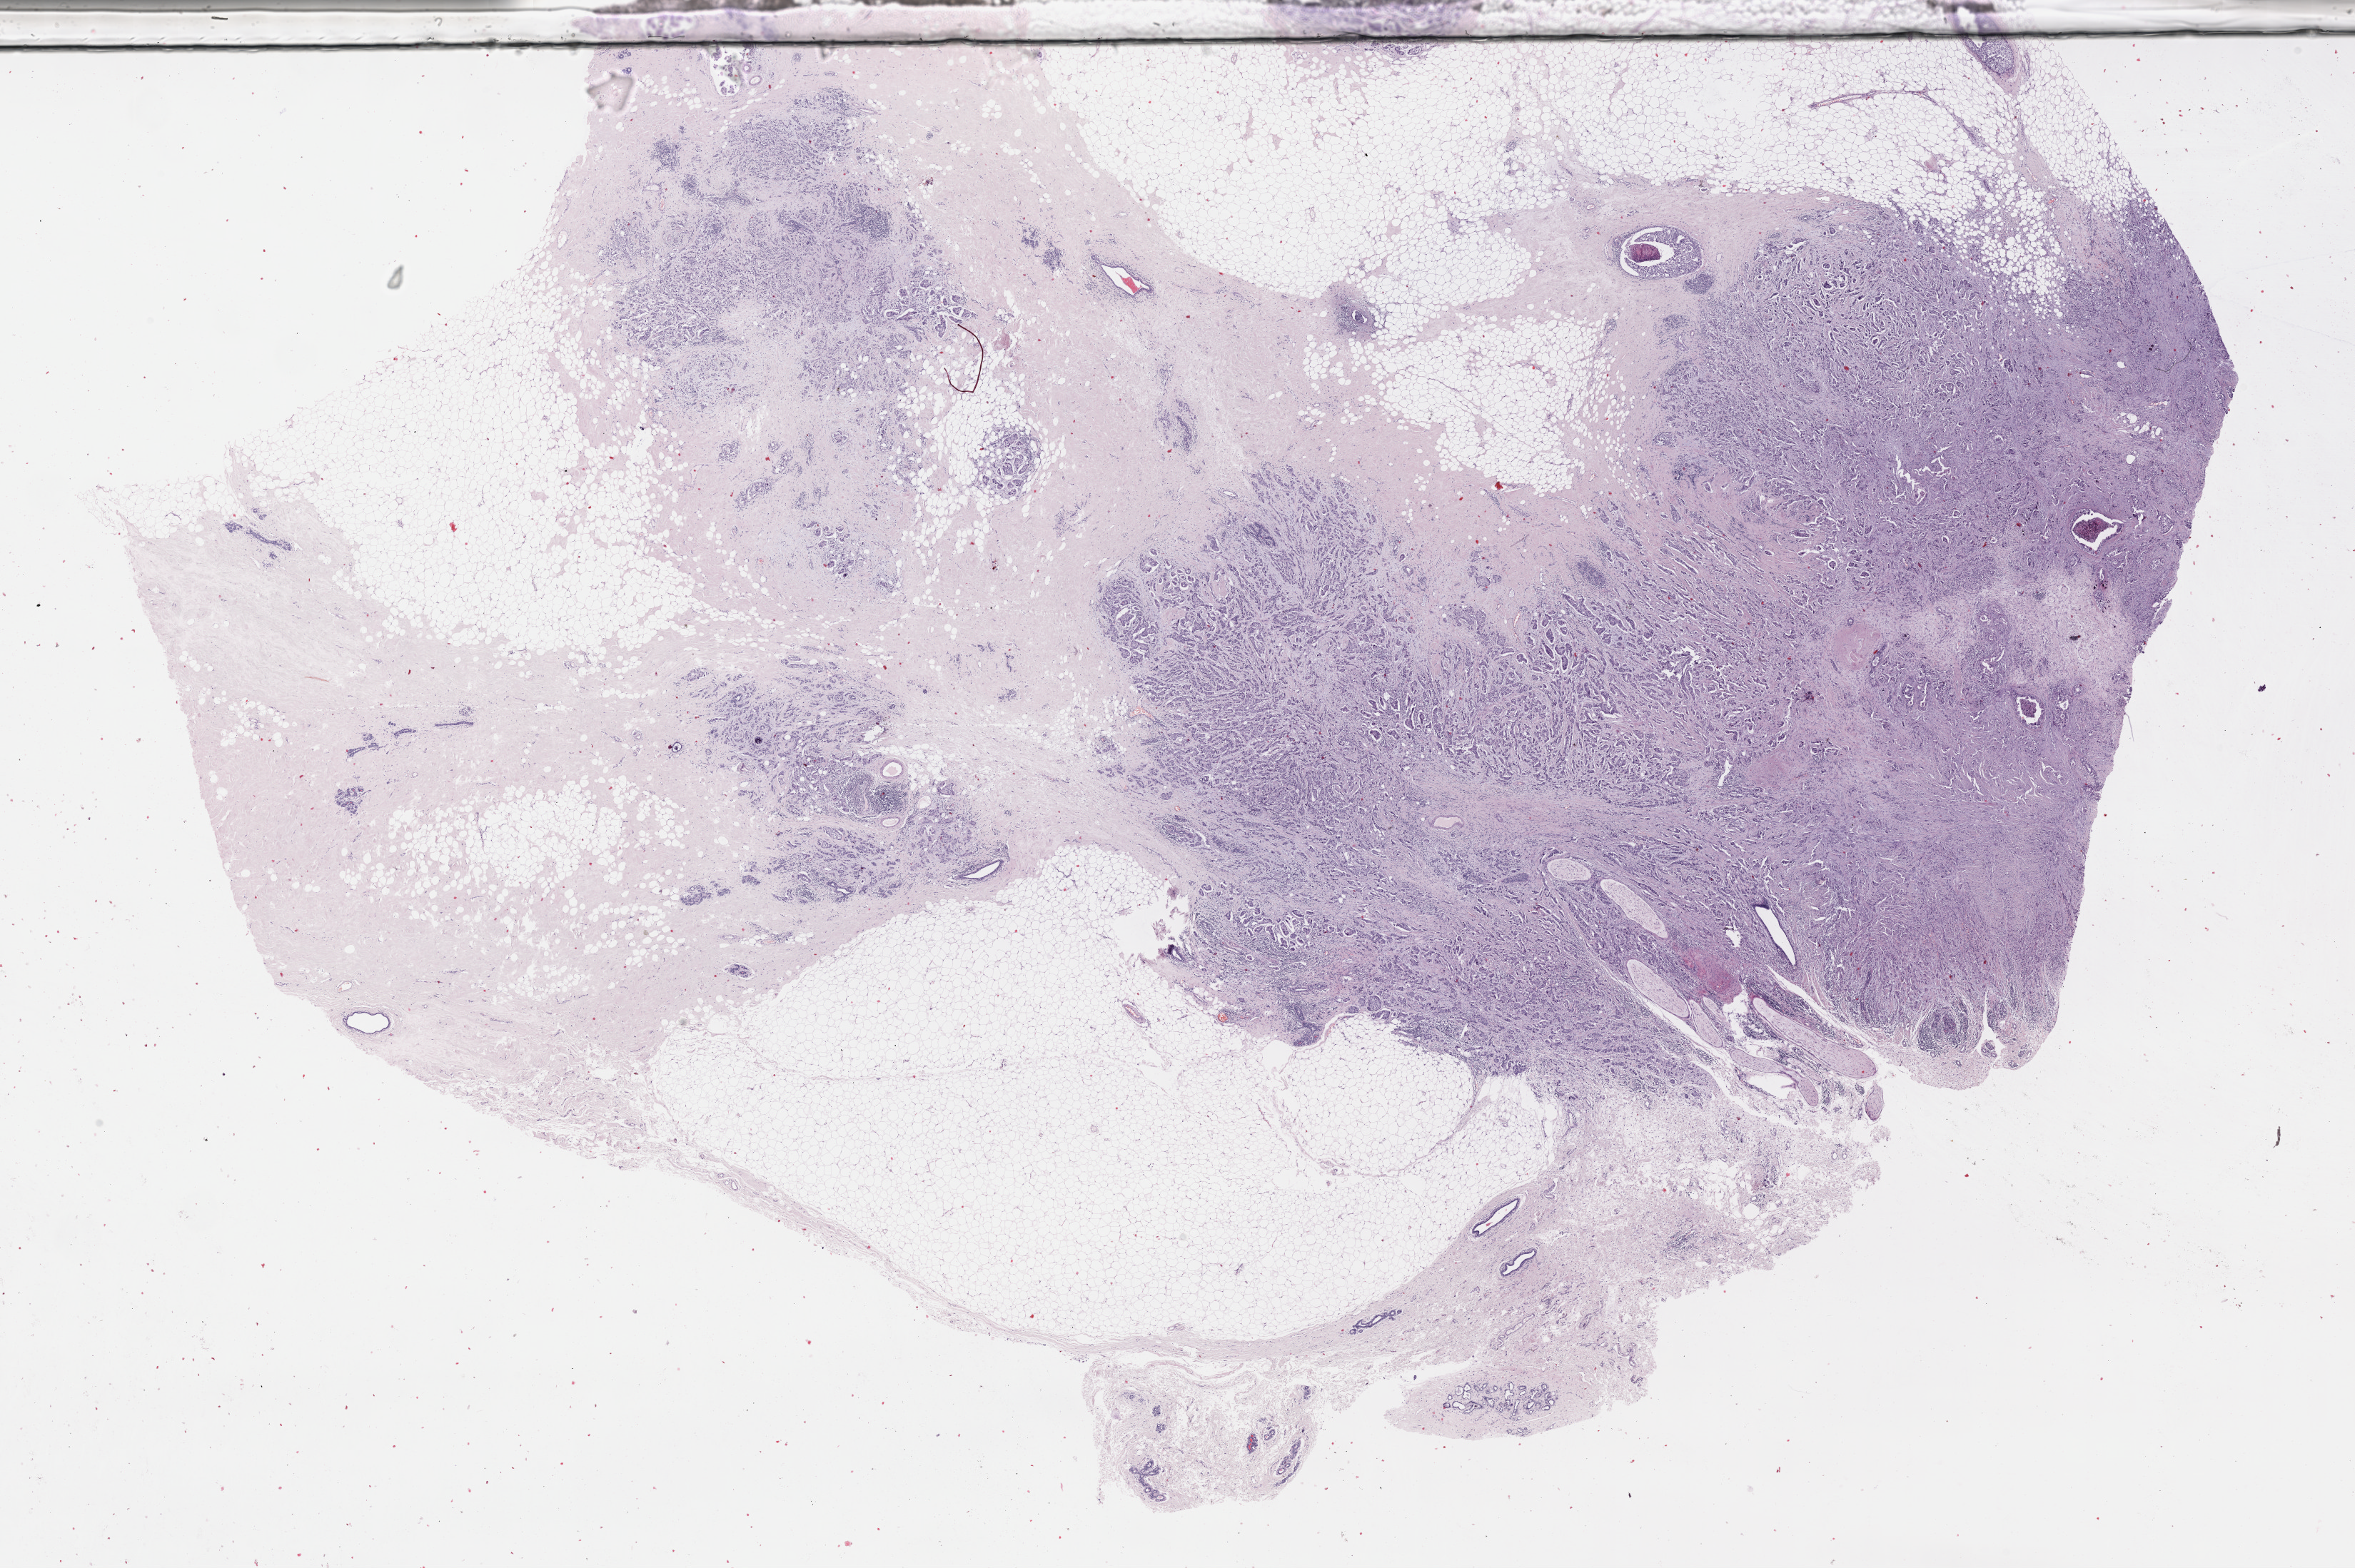
Whole-slide histology image, H&E-stained — a low-resolution overview of the entire scanned area, about 26.7 x 17.8 mm. Formalin-fixed paraffin-embedded (FFPE) diagnostic section. Primary tumour sample from the breast. Female, age 59 years at initial diagnosis.
Laterality: left. TNM: T2 N2a M0. AJCC pathologic stage: IIIA (7th edition). Diagnosis: Infiltrating duct carcinoma, NOS.